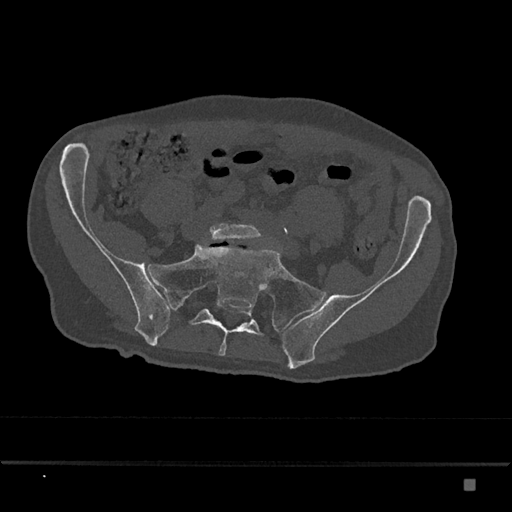
CT including the spine, one axial slice. Position 213 of 797 along the scan axis. Reconstruction kernel Br40s/3. 120 kVp. Bone window (W 1800 / L 400 HU). 512 × 512 image matrix, field of view 390 × 390 mm. Male patient, age 72 years. From the clinical record (not read from this slice): primary cancer: prostate.
Outlined on this slice (semi-automatically segmented with operator editing):
- L5 vertebra: bounding box [x1, y1, x2, y2] px = [210, 223, 262, 241]